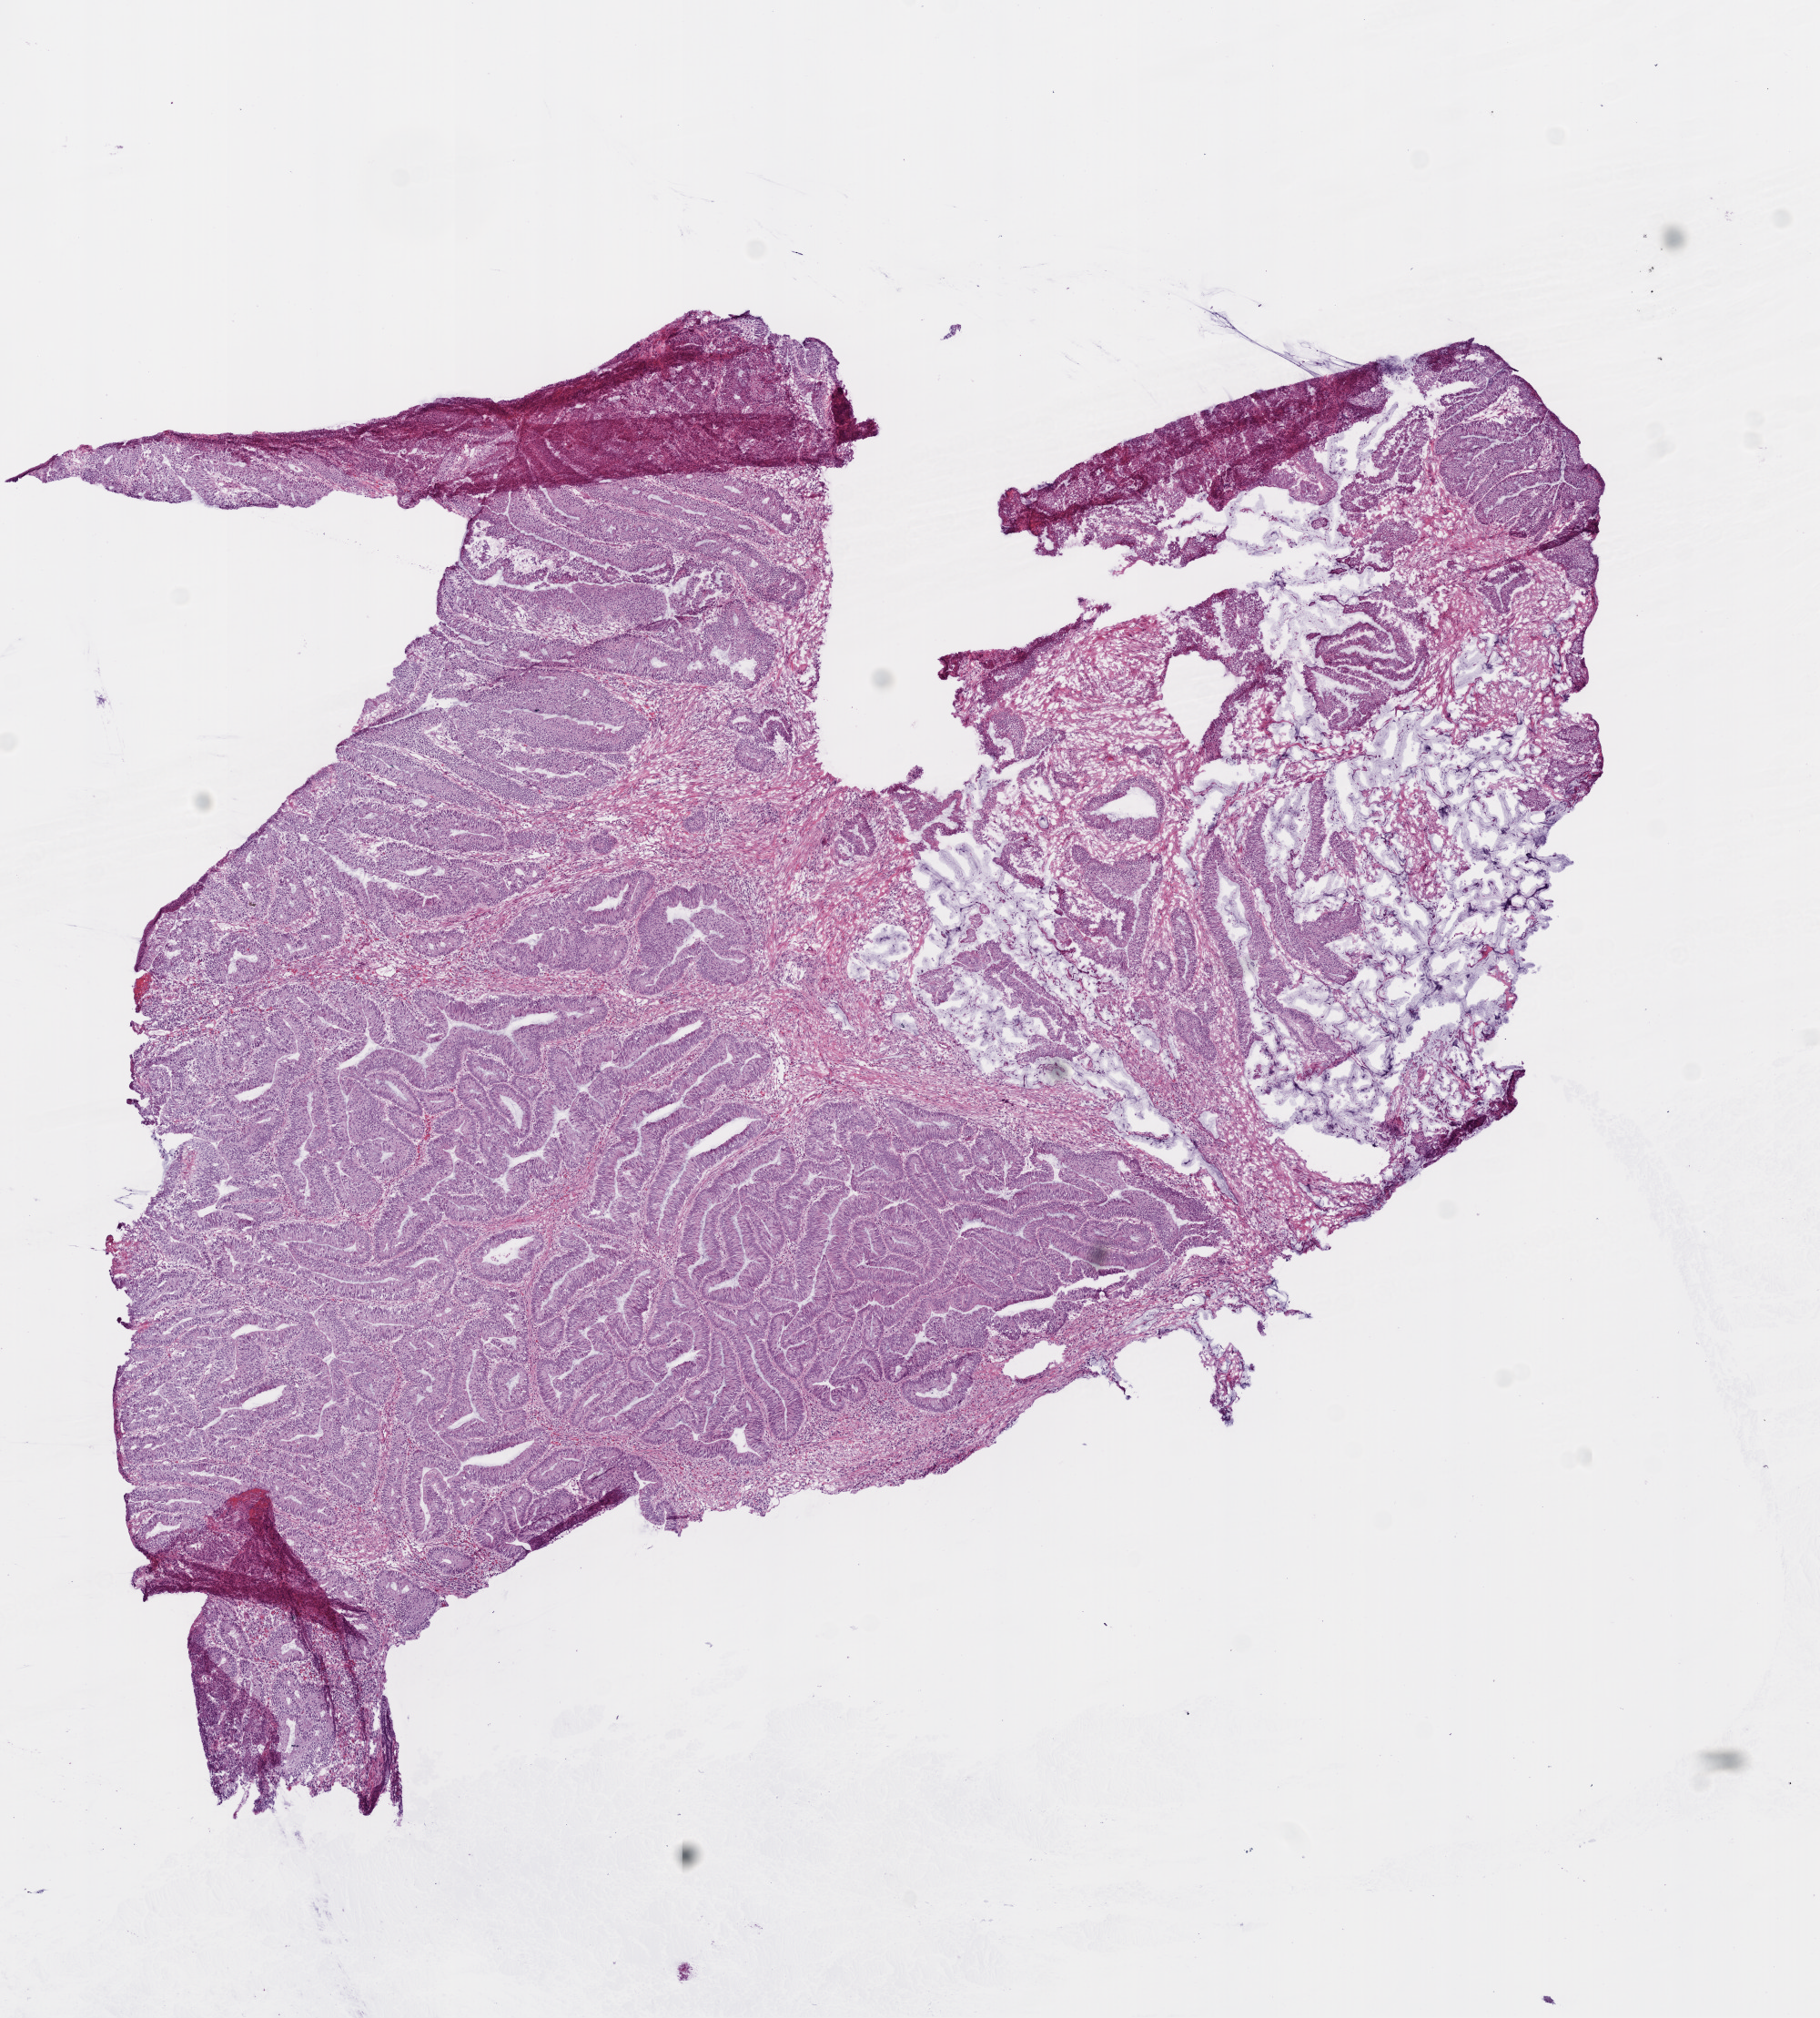
Digitized H&E-stained tissue section (whole slide) — a low-resolution overview of the entire scanned area, about 8.0 x 8.9 mm. Frozen section from the top of the tissue portion. Colon, primary tumour sample. Male patient; age at initial diagnosis 88 years. Pathologist review of this section (percent, as recorded): tumour cells 85%, tumour nuclei 85%, normal cells 0%, stromal cells 15%, necrosis 0%.
Diagnosis: Mucinous adenocarcinoma. Lymph nodes positive (case pathology): 0 of 13 examined. AJCC pathologic stage: IIA.